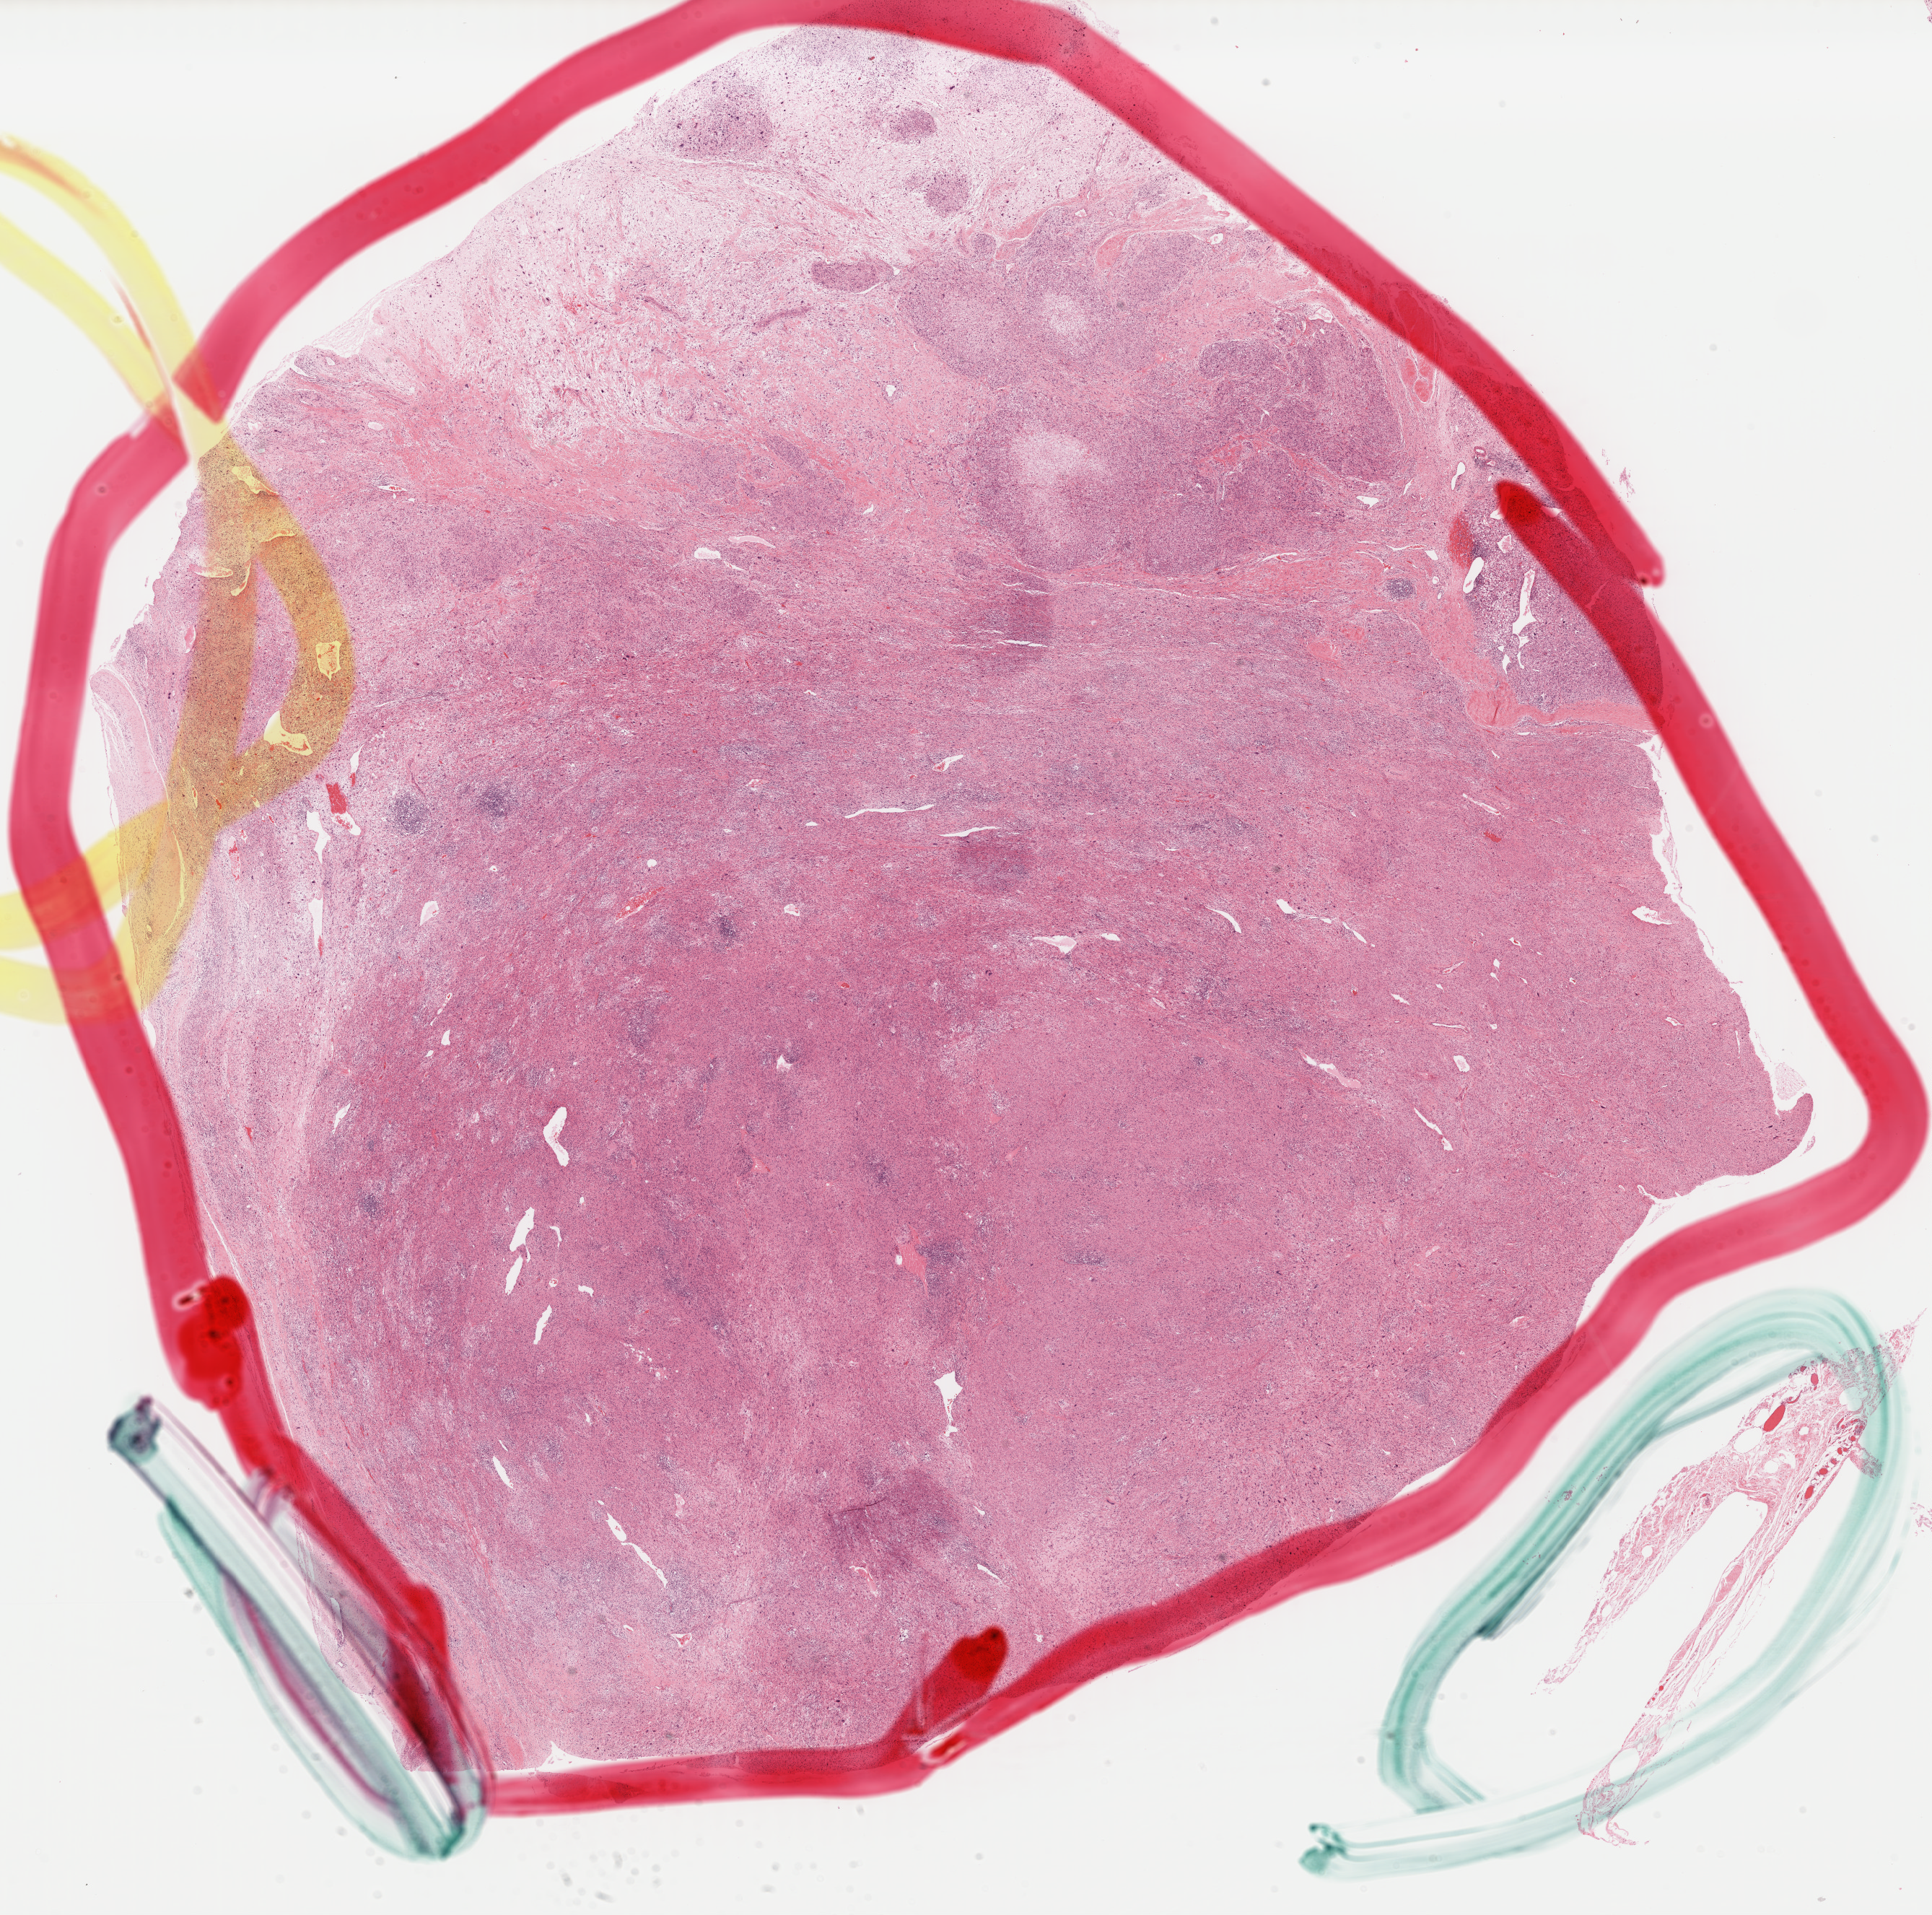
H&E-stained whole-slide image, a low-resolution overview of the entire scanned area, about 21.1 x 20.9 mm. Formalin-fixed paraffin-embedded (FFPE) diagnostic section. Sample: primary tumour, connective, subcutaneous and other soft tissues. Female, age 50 years at initial diagnosis.
Histologic diagnosis: Pleomorphic liposarcoma (connective, subcutaneous and other soft tissues of head, face, and neck).